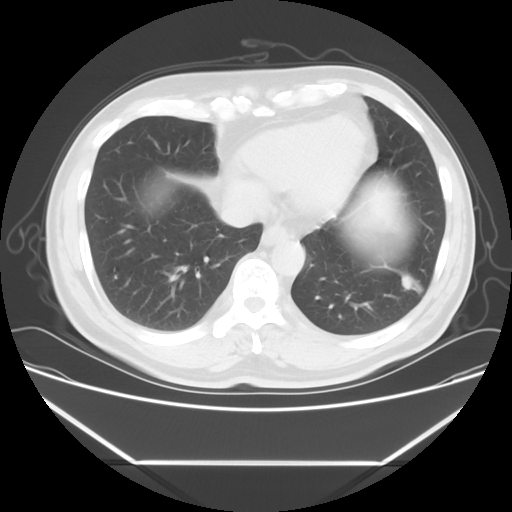
Chest CT, one axial slice. Slice 18 of 57 in the series (ordered by position). Reconstruction kernel STANDARD. Lung window (W 1500 / L -600 HU). 512 × 512 image matrix. Patient: male, 53 years. From the clinical record (not read from this slice): clinical TNM (as recorded): T1c N0 M0; histopathological grade: G2-3.
Annotated regions visible in this slice (bounding box drawn by a radiologist):
- lung tumour (recorded histology: adenocarcinoma): bounding box <398,267,423,302> (left, top, right, bottom; pixels)